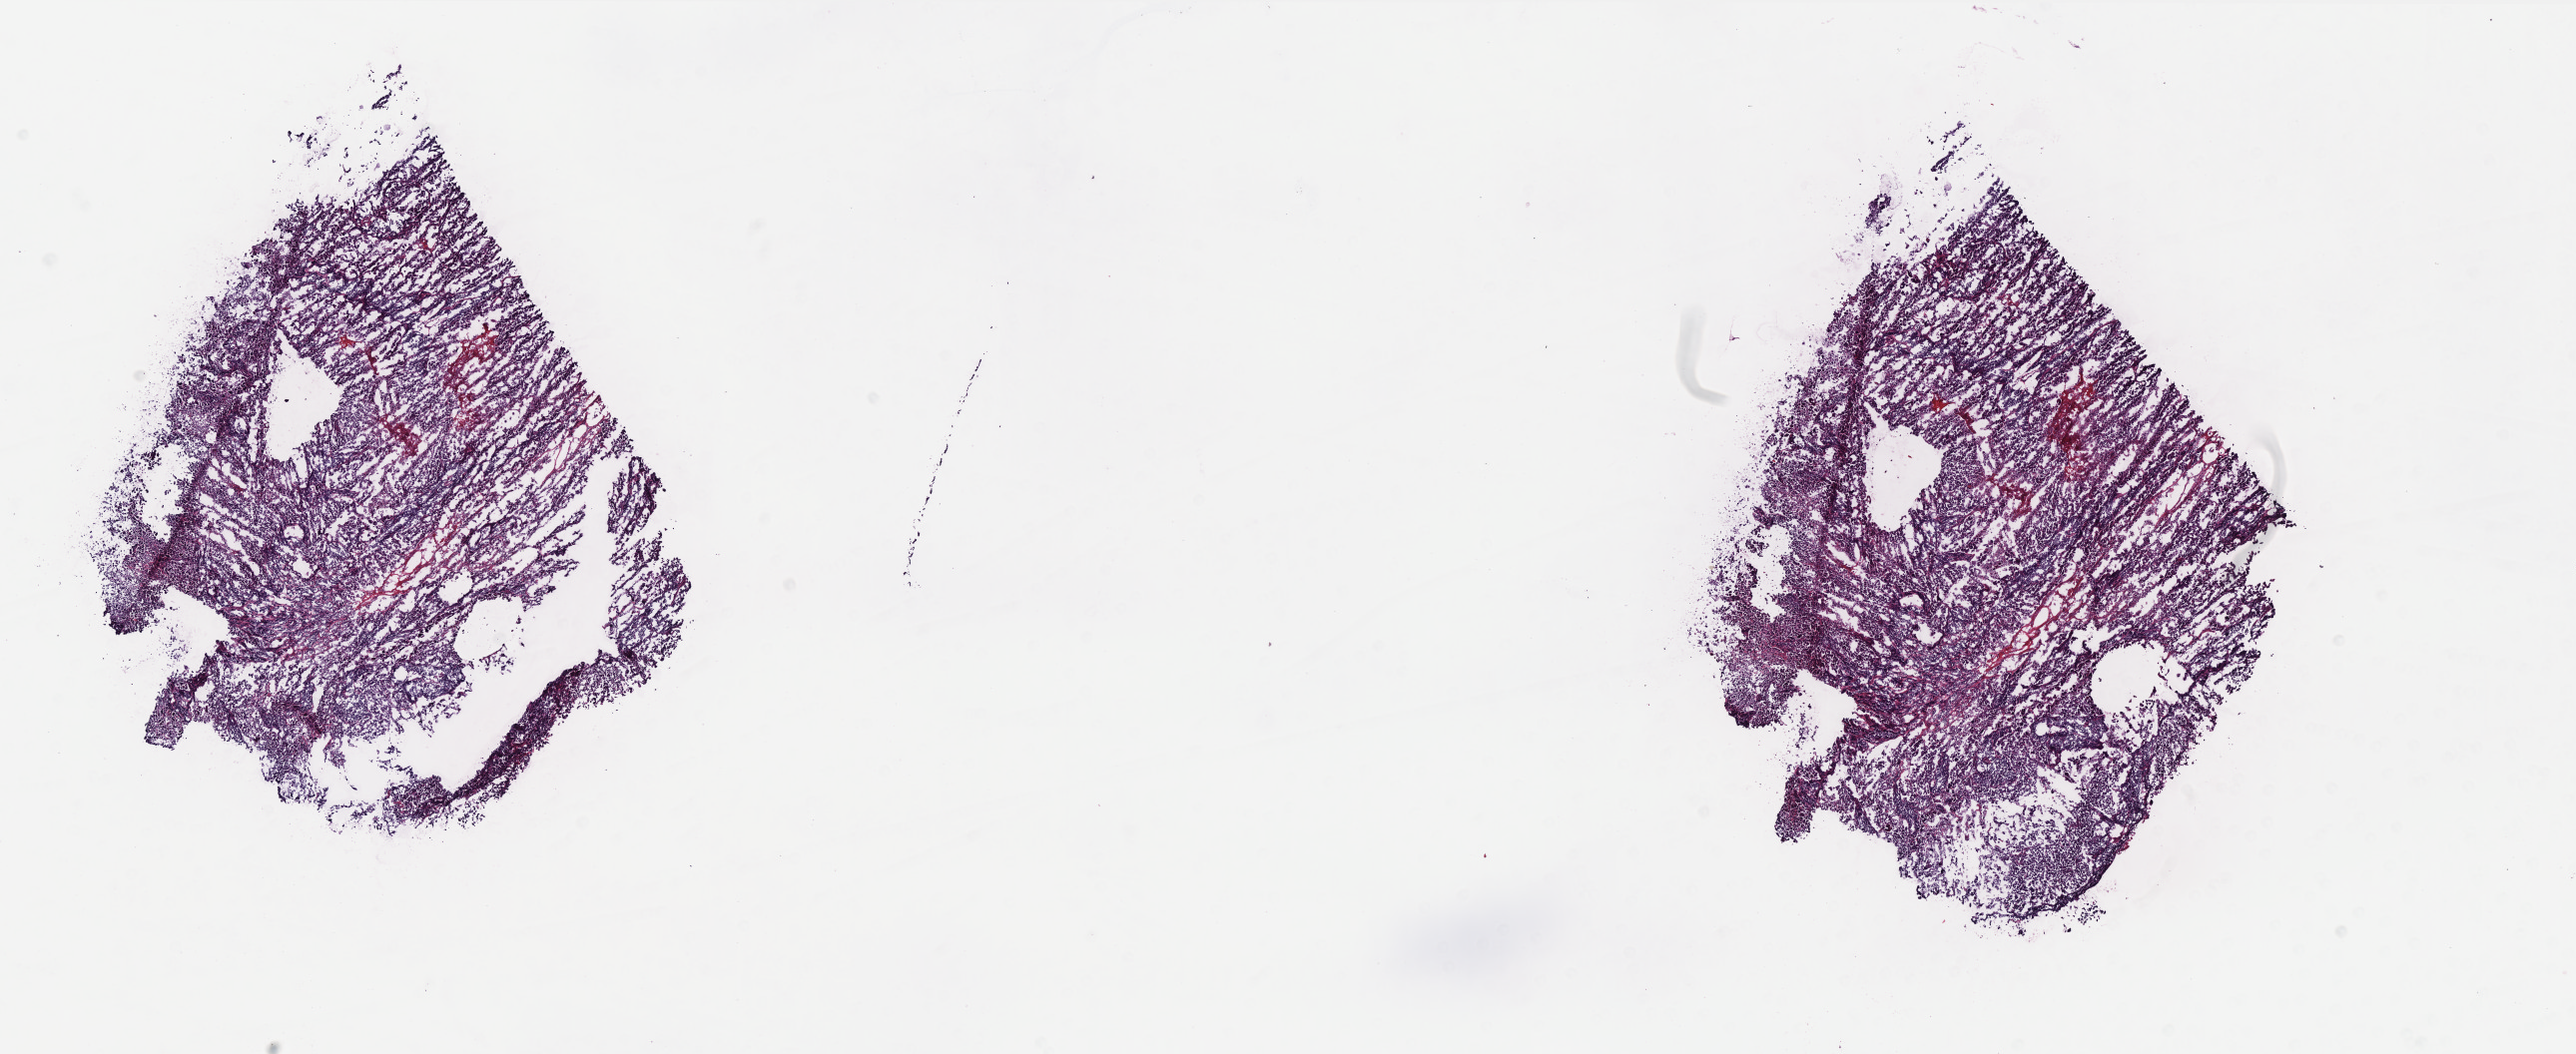
Whole-slide histology image, Hematoxylin and eosin (H&E) stained — low-resolution overview of the scanned area, about 20.7 x 8.5 mm (from a 40x scan), frozen section, sample: primary tumour, uterus. Patient sex: female. Histologic grade: G3 (poorly differentiated). Slide review estimates, as recorded: tumour cells 100%, tumour nuclei 60%, normal cells 0%, stromal cells 0%, necrosis 0%. Inflammatory infiltration, as recorded: lymphocyte infiltration 0%, monocyte infiltration 0%, neutrophil infiltration 0%.
Lymph nodes positive (case pathology): 0 of 10 examined. FIGO stage: IVB. Pathologic diagnosis: Endometrioid adenocarcinoma, NOS (endometrium).